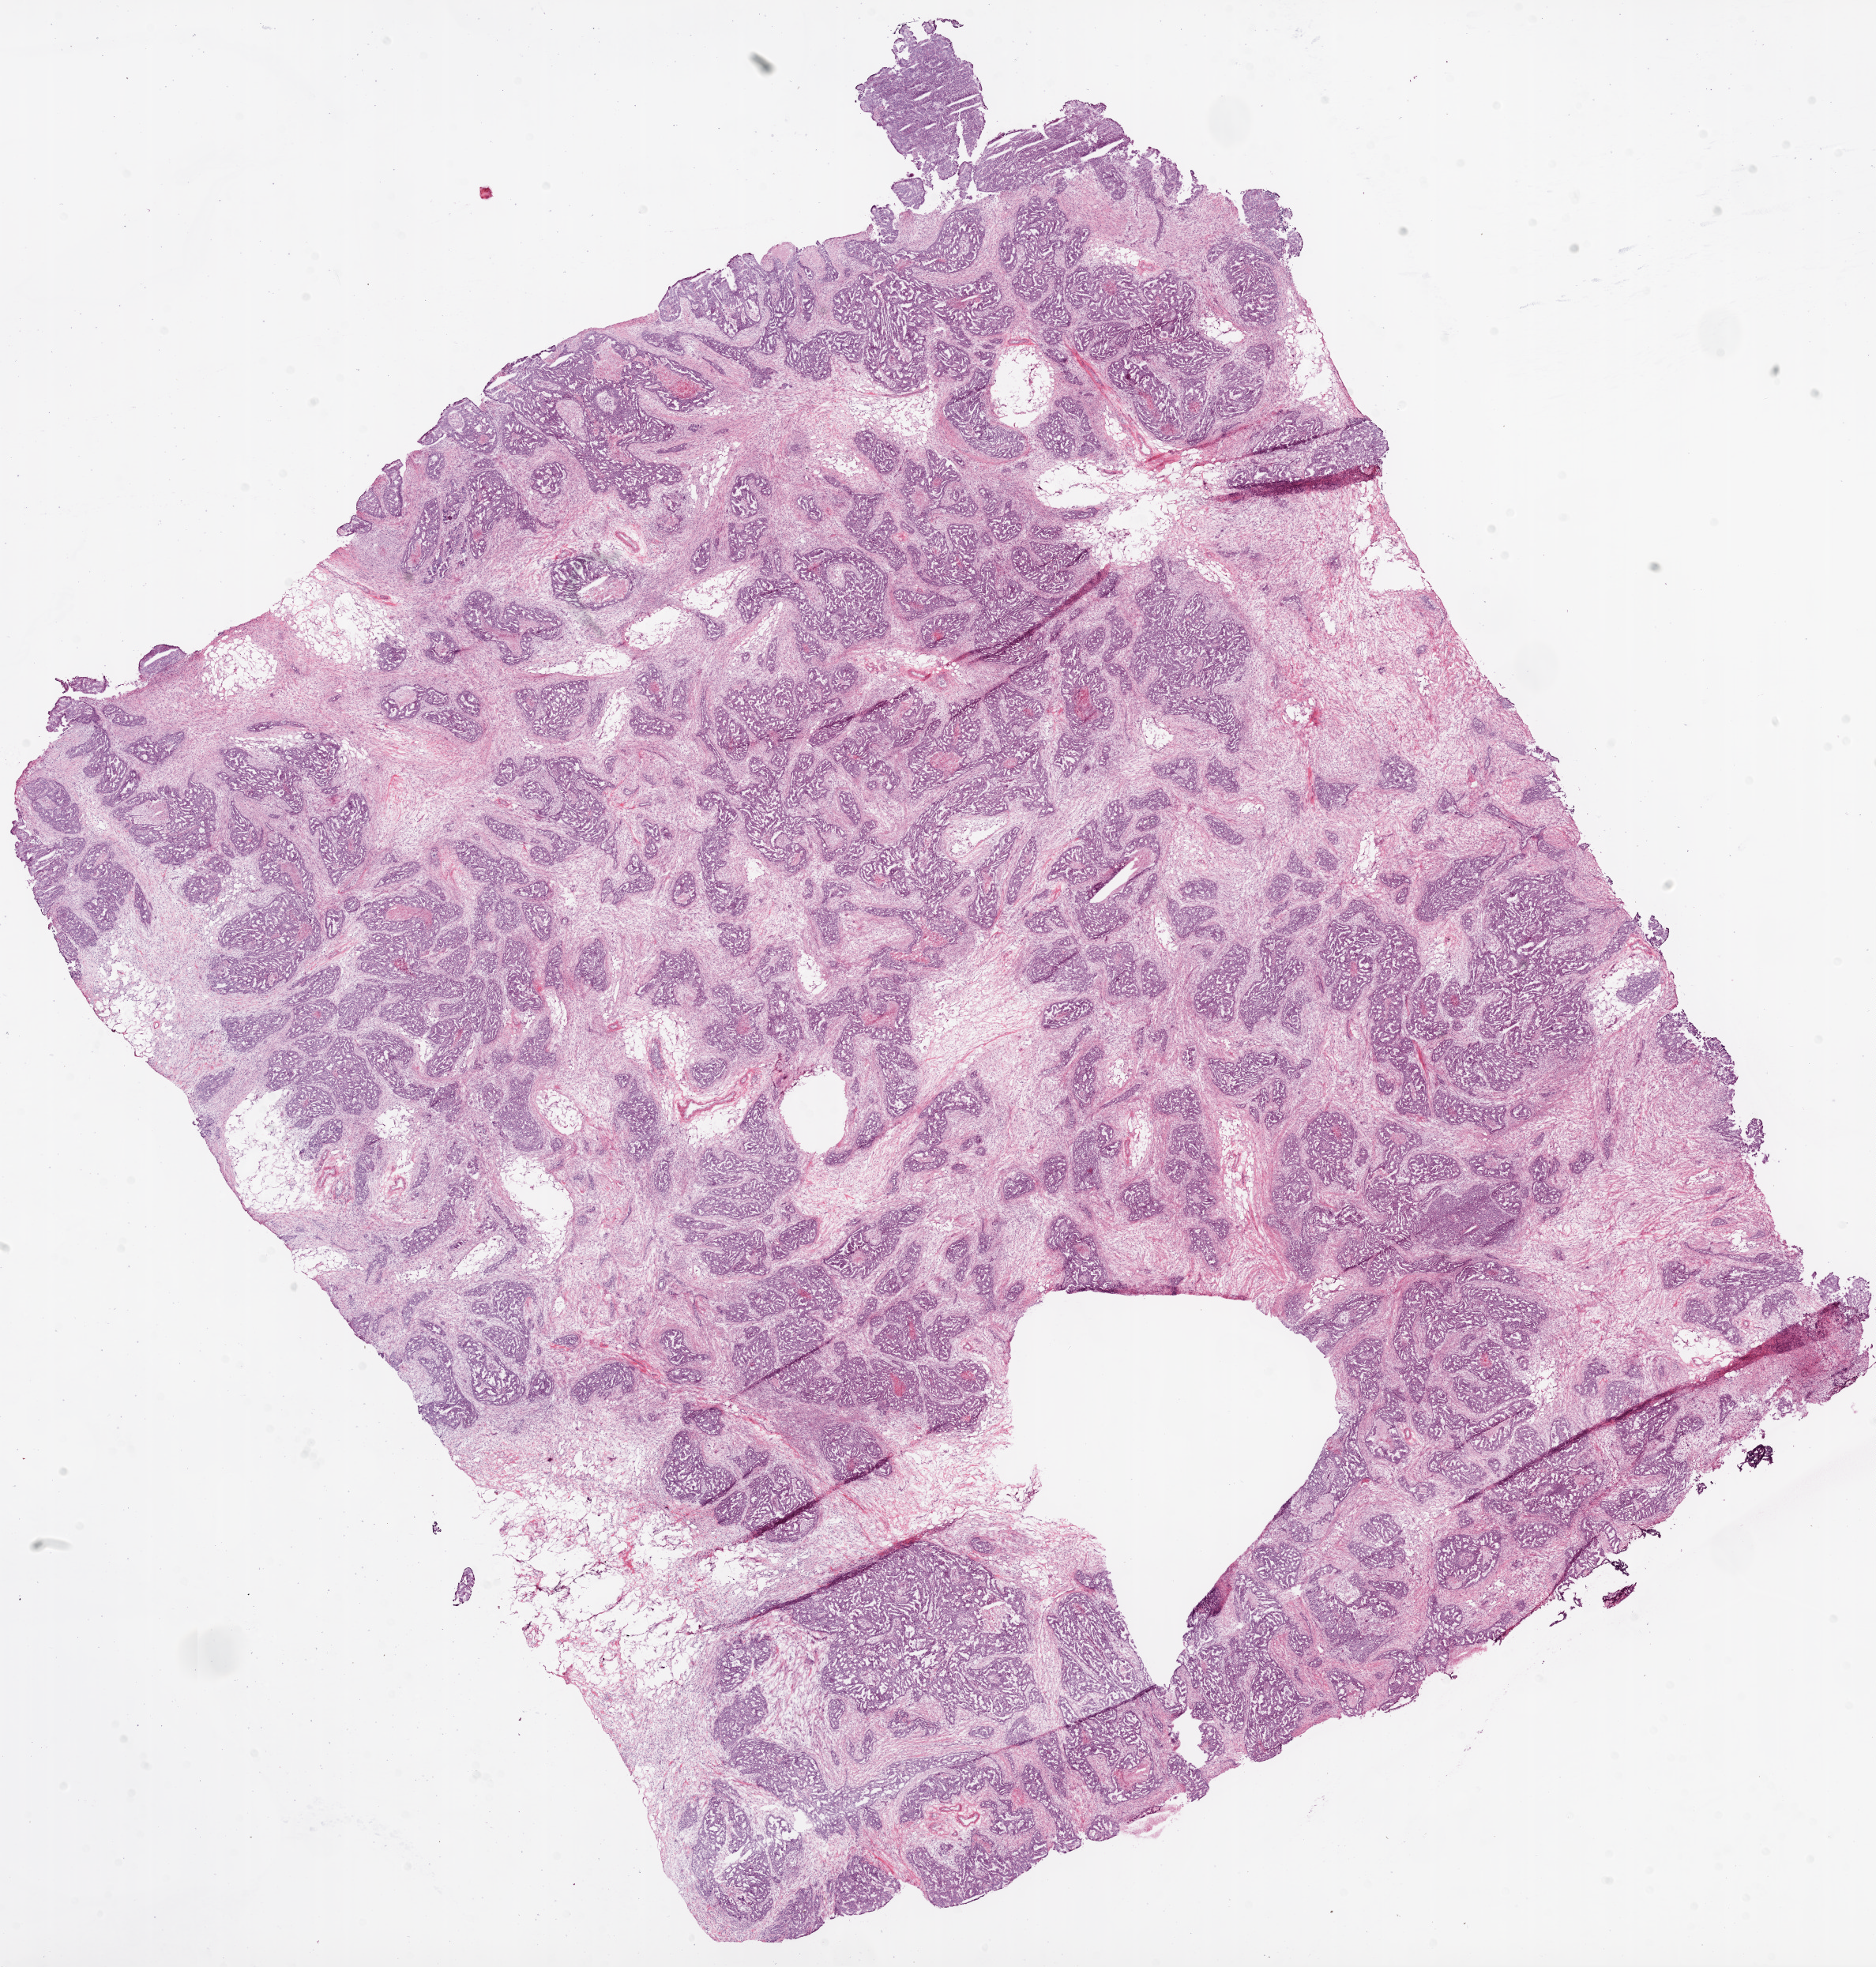
Hematoxylin and eosin (H&E) stained whole-slide image — low-resolution overview of the scanned area, about 19.1 x 20.0 mm. Frozen section from the bottom of the tissue portion. Sample: primary tumour, ovary. Female, age 71 years at initial diagnosis. Histologic grade: G3 (poorly differentiated). Composition of this section per pathologist review: tumour cells 80%, tumour nuclei 85%, normal cells 0%, stromal cells 15%, necrosis 5%.
FIGO stage: IIIC. Histologic diagnosis: Serous cystadenocarcinoma, NOS.